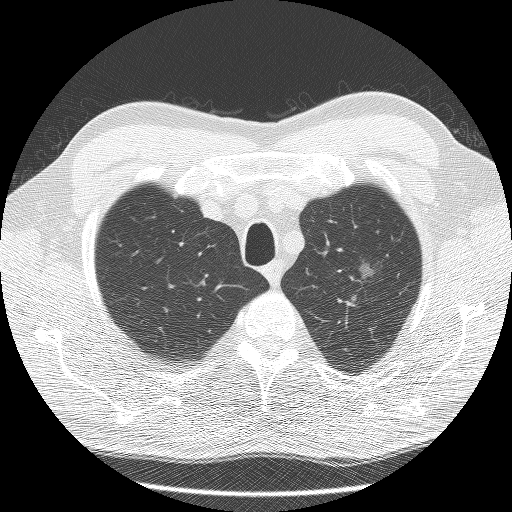
Chest CT (low-dose screening protocol), one axial image, third screening round (two years after baseline), lung window (W 1500 / L -600 HU), slice 20 of 132 in the series. Male participant, aged 60 years at enrolment. Former smoker at enrolment.
• Lesion marked by an expert reader, bounding box <334,250,392,301> (left, top, right, bottom; pixels).
• The screening reader recorded 2 non-calcified nodules or masses ≥4 mm on this exam (right lower lobe, left upper lobe); which of them this box marks is not recorded.
• Official screen result: positive, other.
• Participant outcome: lung cancer diagnosed 99 days after this screen — bronchiolo-alveolar carcinoma, non-mucinous, left upper lobe, well differentiated (G1), stage IA (AJCC 6th edition), 16 mm at pathology.